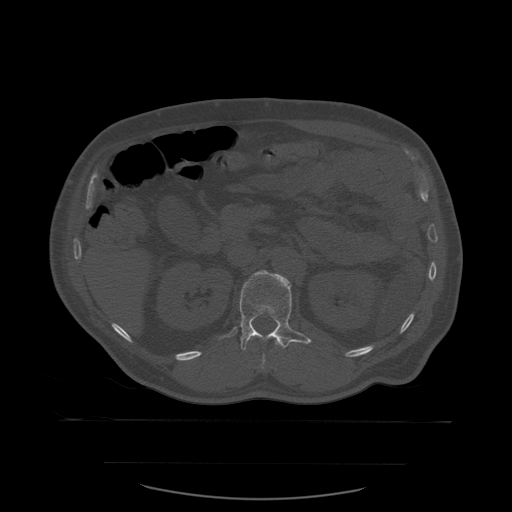
CT including the spine, one axial slice; slice 249 of 590 in the series (ordered by position); bone window (W 1800 / L 400 HU); 1.25 mm slice thickness; 512 × 512 image matrix, field of view 479 × 479 mm. Patient age 71 years. Case-level facts recorded for this patient, not image findings: primary cancer: lung; vertebrae with lytic lesions (as recorded): T1, T2, L5, S1.
Annotated regions visible in this slice (semi-automatically segmented with operator editing):
- L1 vertebra: bounding box <219,271,312,369> (left, top, right, bottom; pixels)
- T12 vertebra: <275,340,285,349>